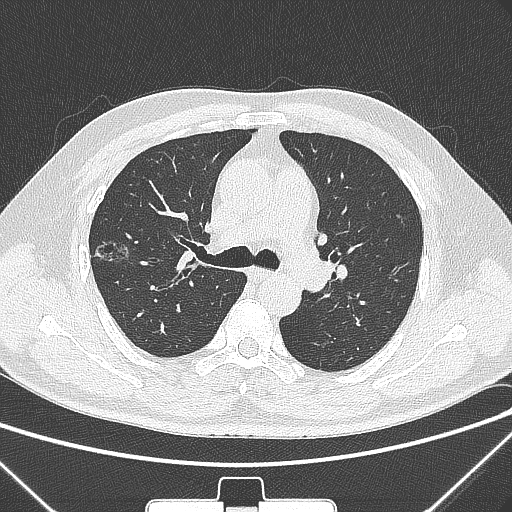
Chest CT, one axial slice. Slice 199 of 320 in the series (ordered by position). 120 kVp. Lung window (W 1500 / L -600 HU). 512 × 512 image matrix. Male patient, age 58 years. From the clinical record (not read from this slice): clinical TNM (as recorded): T1c N0 M0; histopathological grade: G2.
Annotated regions visible in this slice (rectangle marked by the reading radiologist):
- lung tumour (recorded histology: adenocarcinoma): box from (x=89, y=231) to (x=135, y=278) px